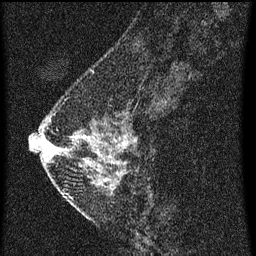
Breast MRI (dynamic contrast-enhanced), one sagittal slice; dynamic contrast-enhanced series, image 2 of 3 at this slice position (ordered by acquisition); 1.5 T; TE 4.2 ms, TR 8 ms; 256 × 256 image matrix, field of view 180 × 180 mm. Patient: female, 47 years.
Annotated regions visible in this slice (semi-automatically segmented with operator editing):
- analysis volume of interest (the breast-tissue region the enhancement analysis was run in; not a lesion): box from (x=42, y=92) to (x=140, y=199) px
- tumour enhancement mask (voxels above the 70 % enhancement threshold inside the analysis volume of interest): (x=47, y=138)–(x=126, y=163)